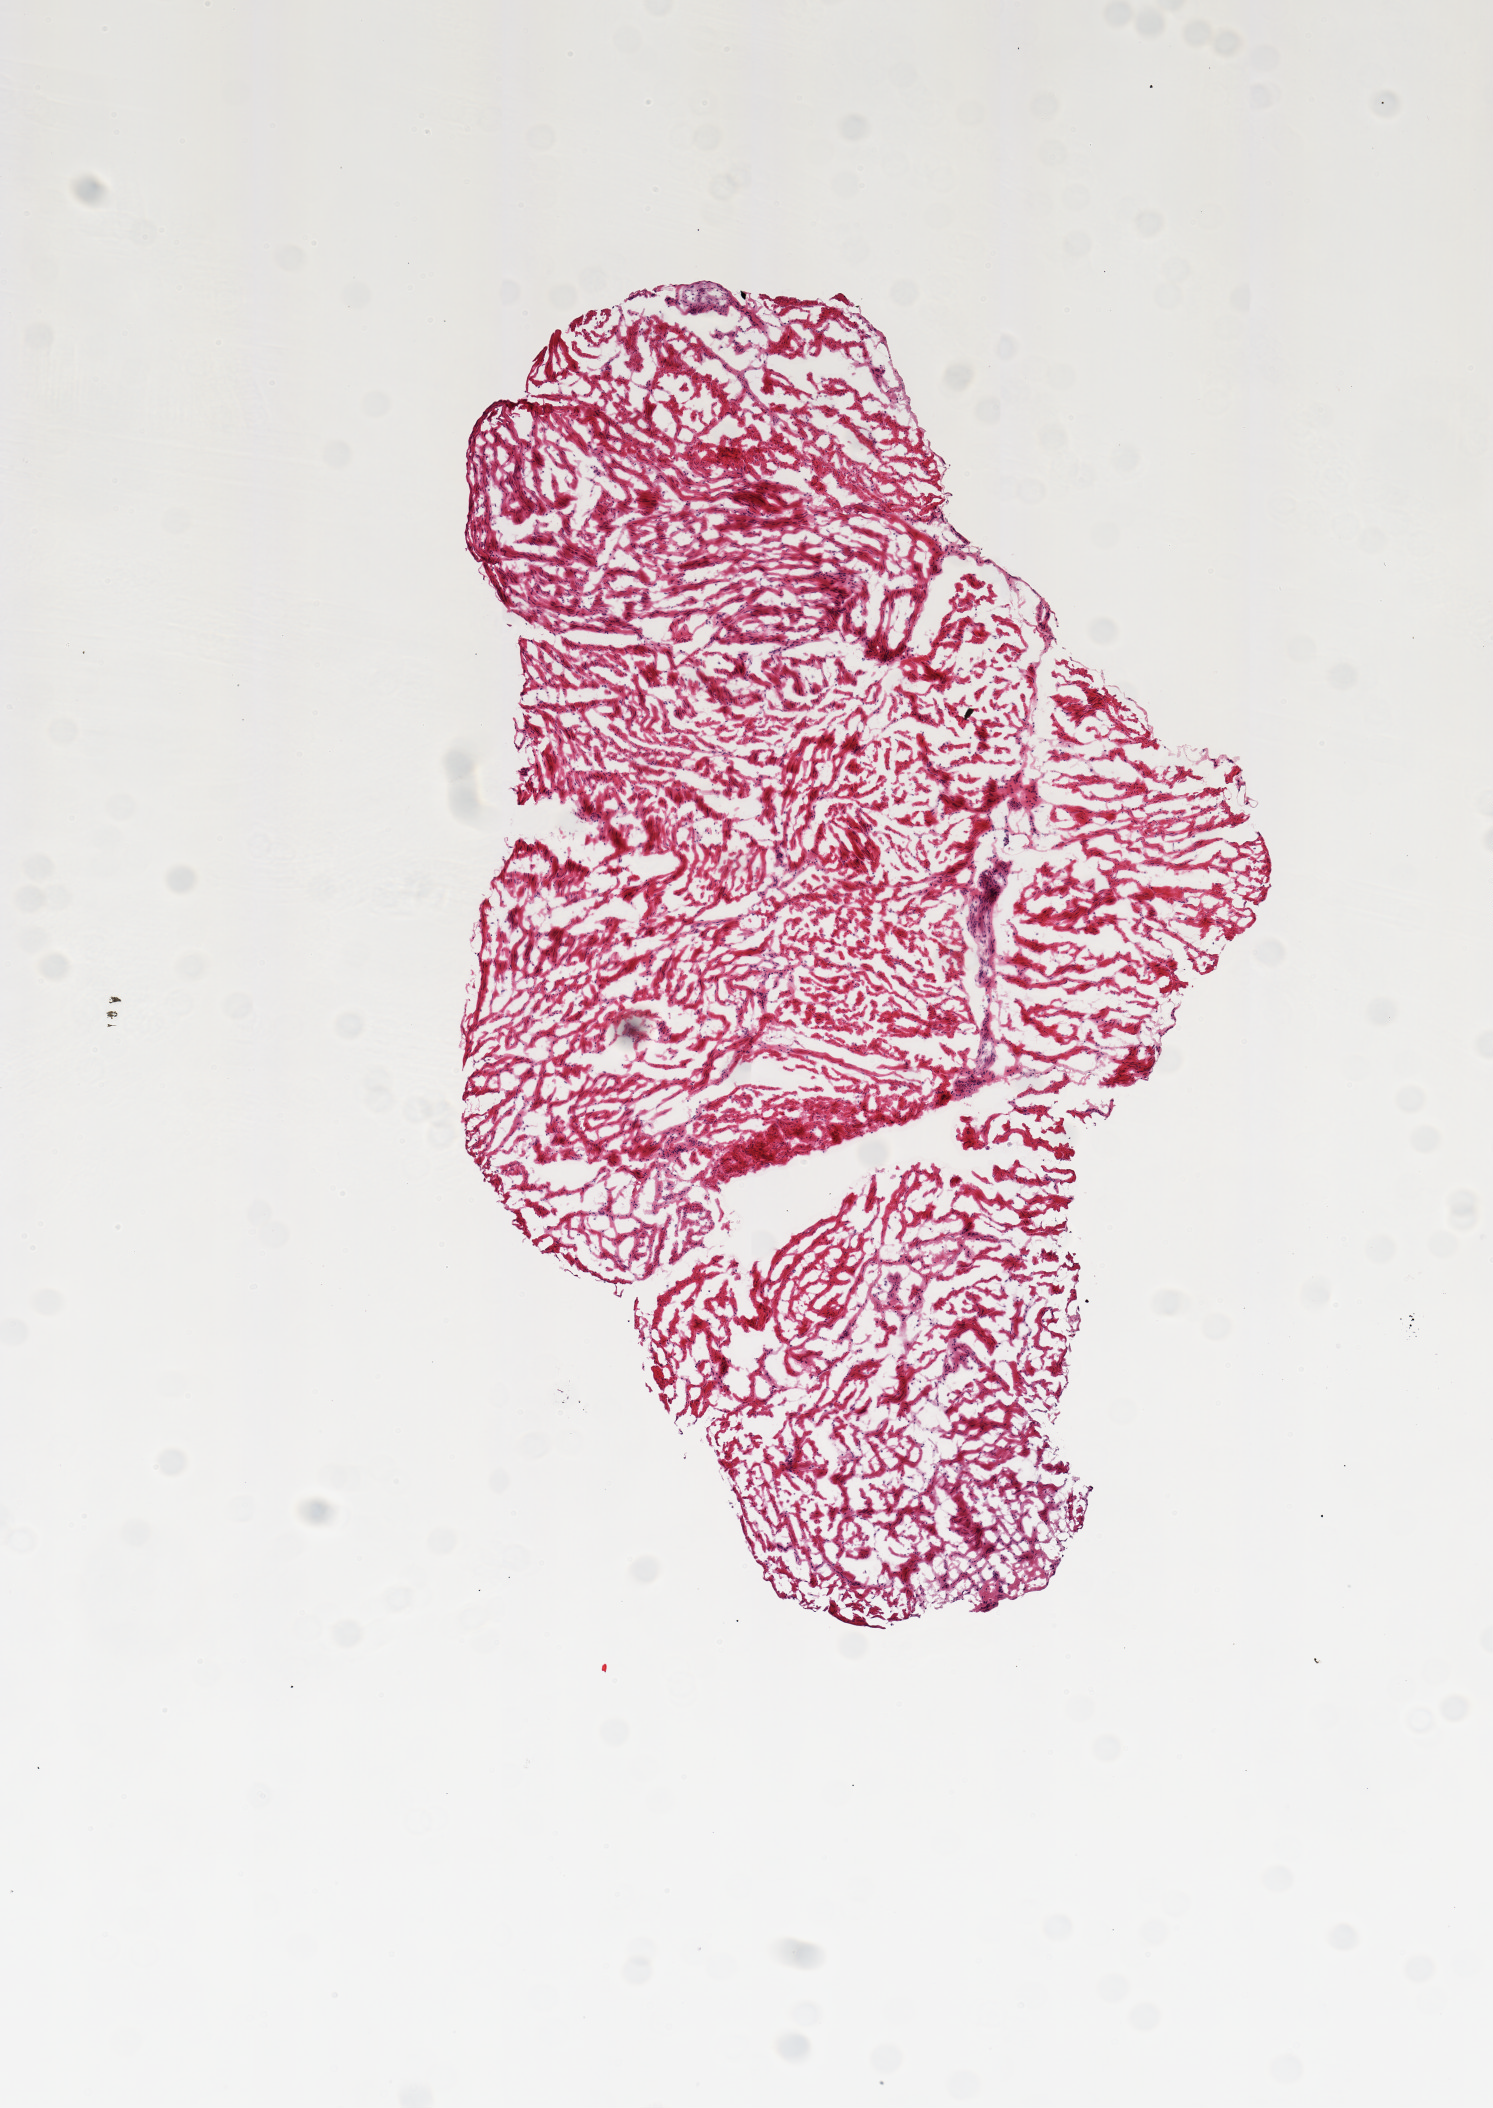
Whole-slide image, haematoxylin and eosin stain, shown as a low-resolution overview of the whole scanned area (about 5.9 x 8.3 mm). Frozen section (dry ice). Sampled site (target tissue): esophageal muscle. Donor tissue sample. Donor sex: male.
Pathologist's review note for this sample: 1 piece.